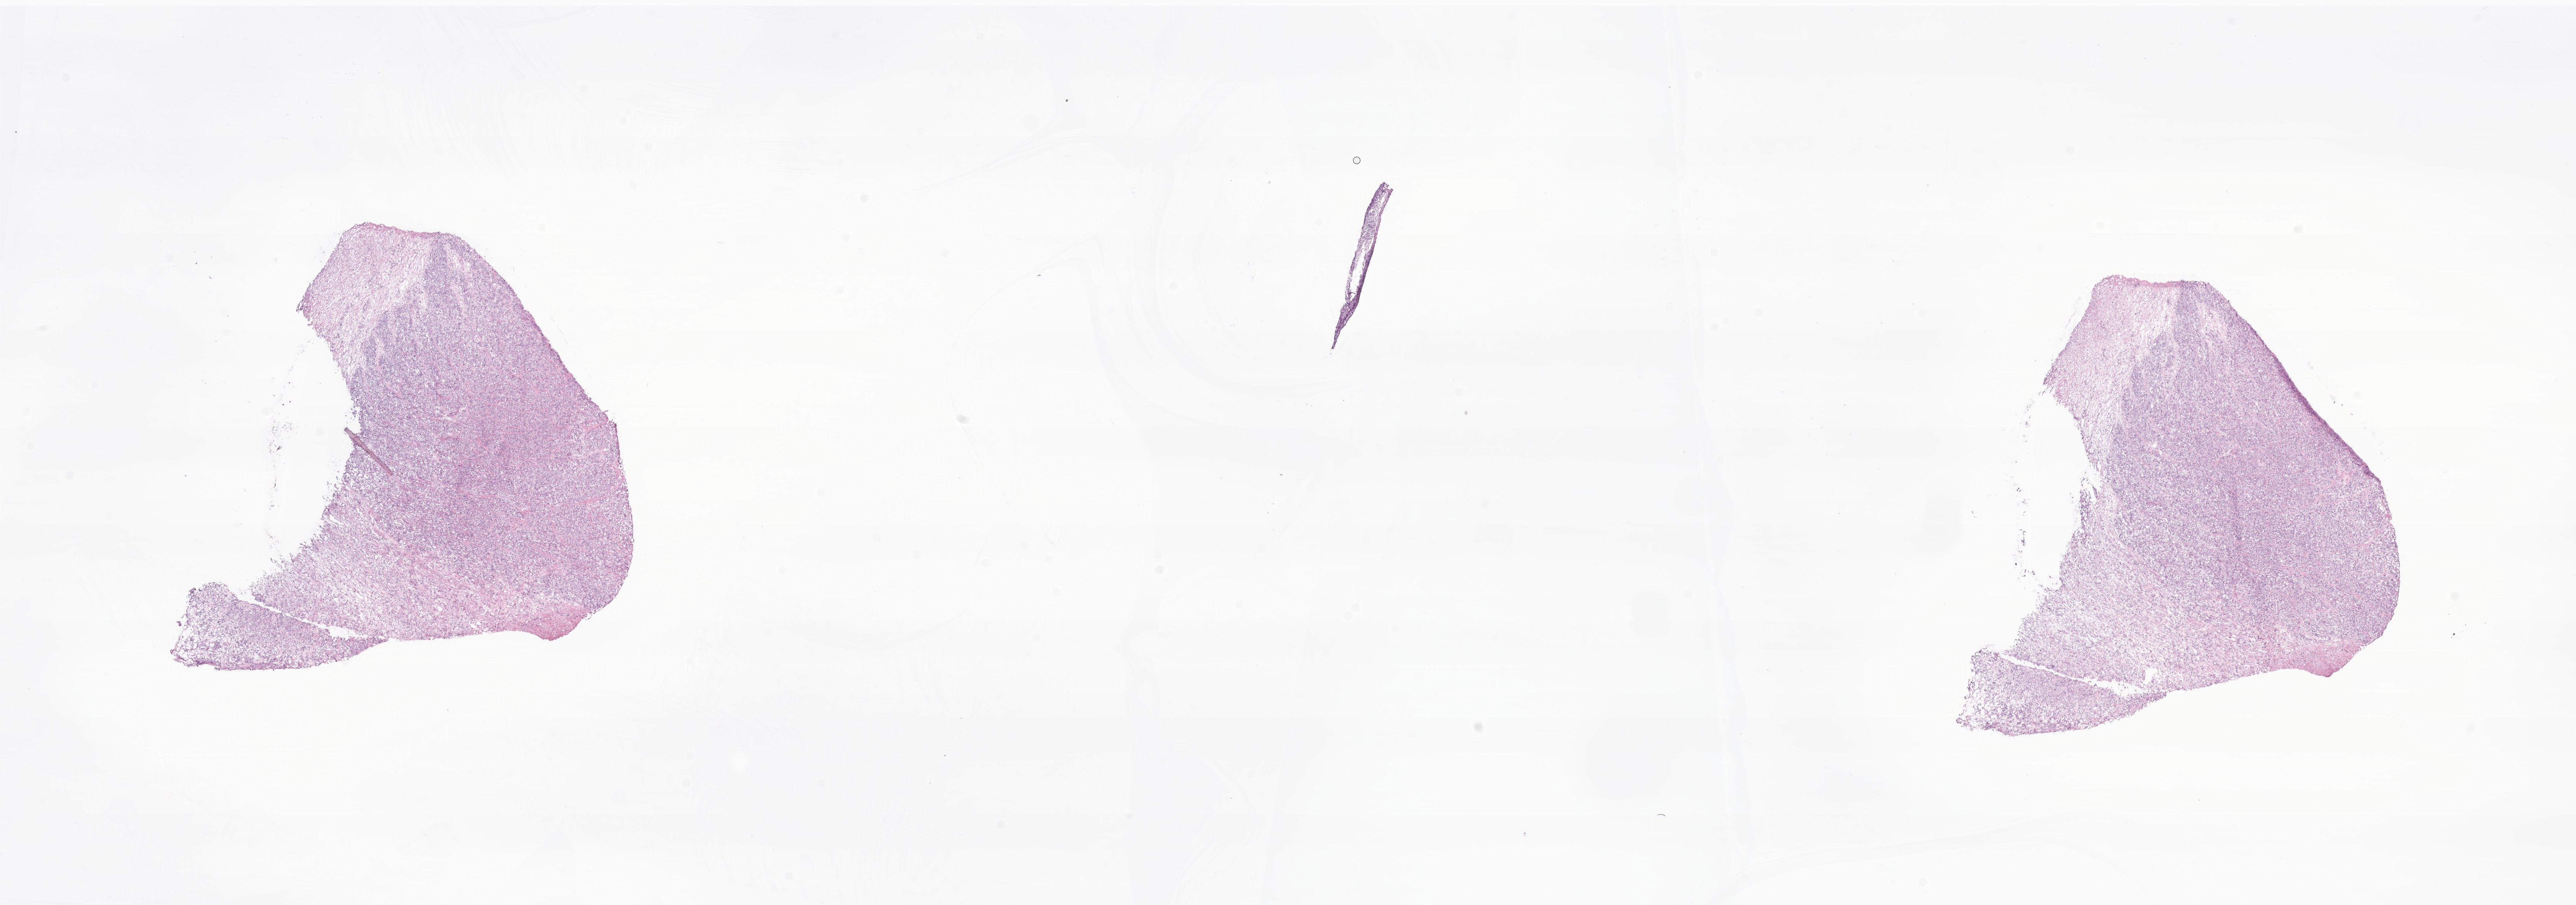
Digitized haematoxylin and eosin-stained section of tumor tissue from the scrotum — low-resolution overview of the scanned area, about 28.4 x 10.0 mm; frozen section (OCT-embedded). Patient: male, age 195 months (16 years 3 months).
Diagnosis (ICD-O-3 morphology term): Rhabdomyosarcoma, NOS.